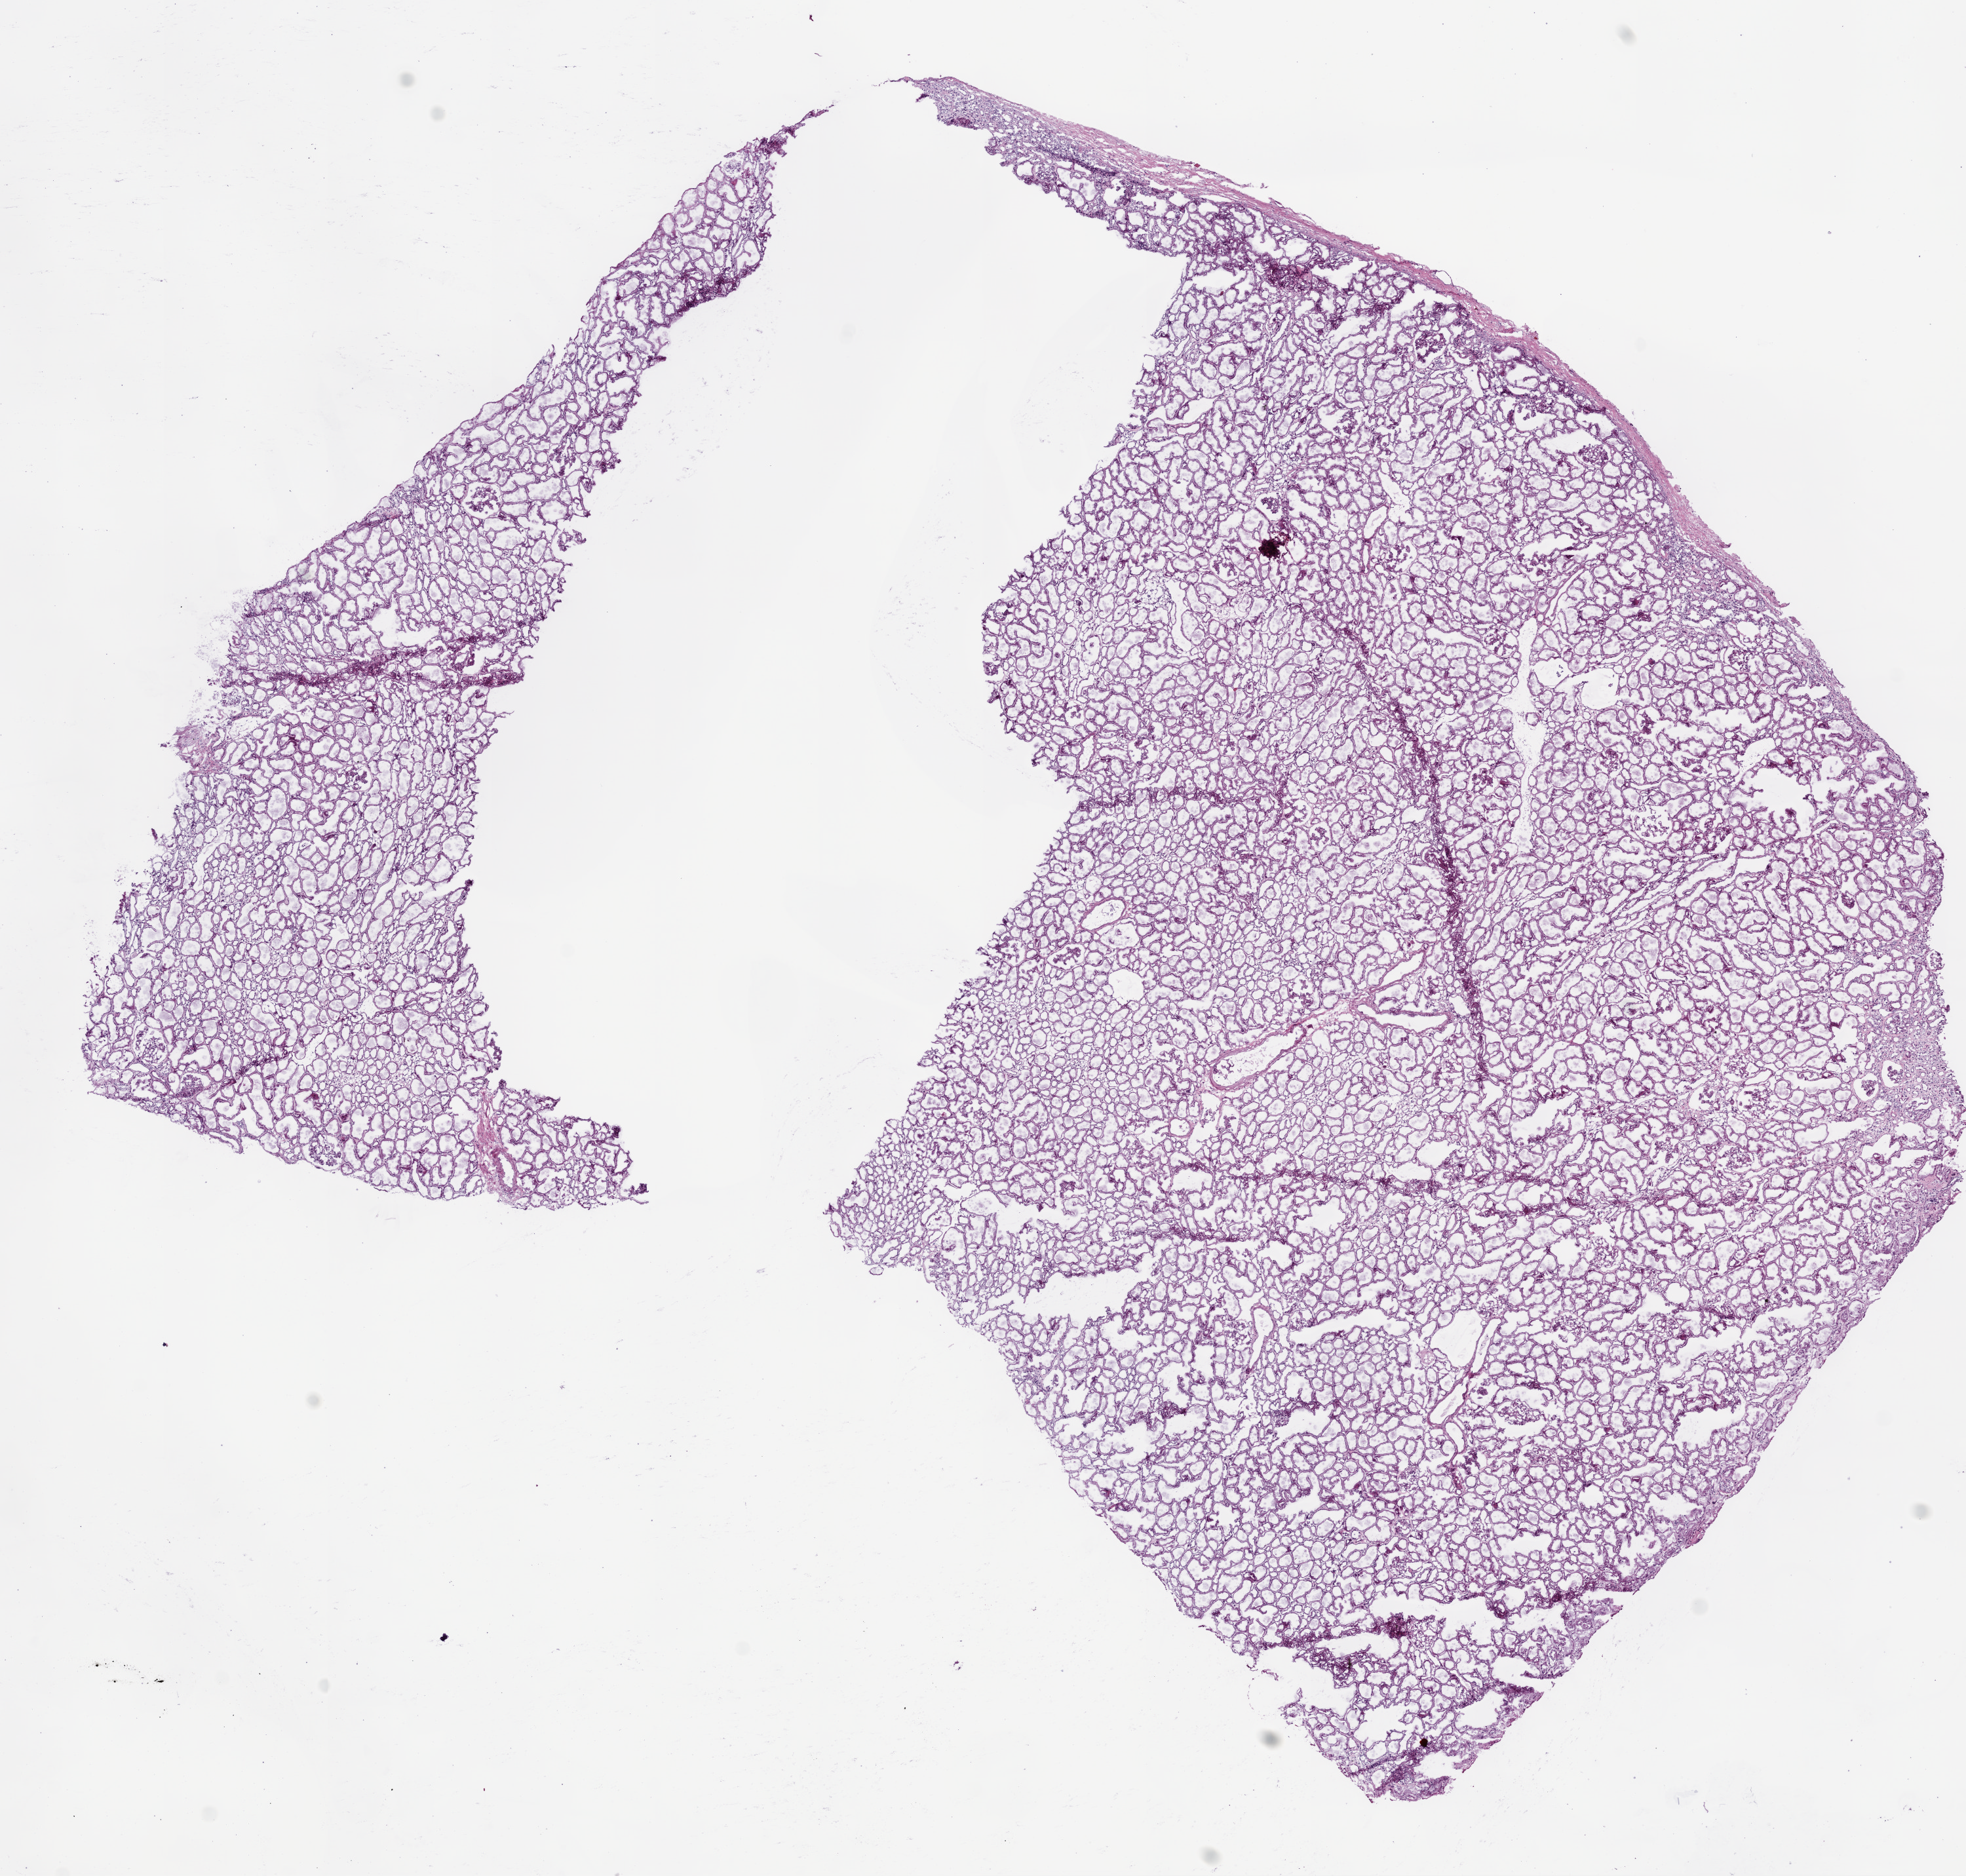
Digitized Hematoxylin and eosin (H&E) stained tissue section (whole slide) — a low-resolution overview of the entire scanned area, about 12.0 x 11.5 mm (from a 20x scan), frozen section from the bottom of the tissue portion, solid tissue normal (non-tumour tissue) sample from the kidney. Female, age 70 years at initial diagnosis.
This section: solid tissue normal (non-tumour) sample from the same patient. Patient diagnosis: Clear cell adenocarcinoma, NOS.